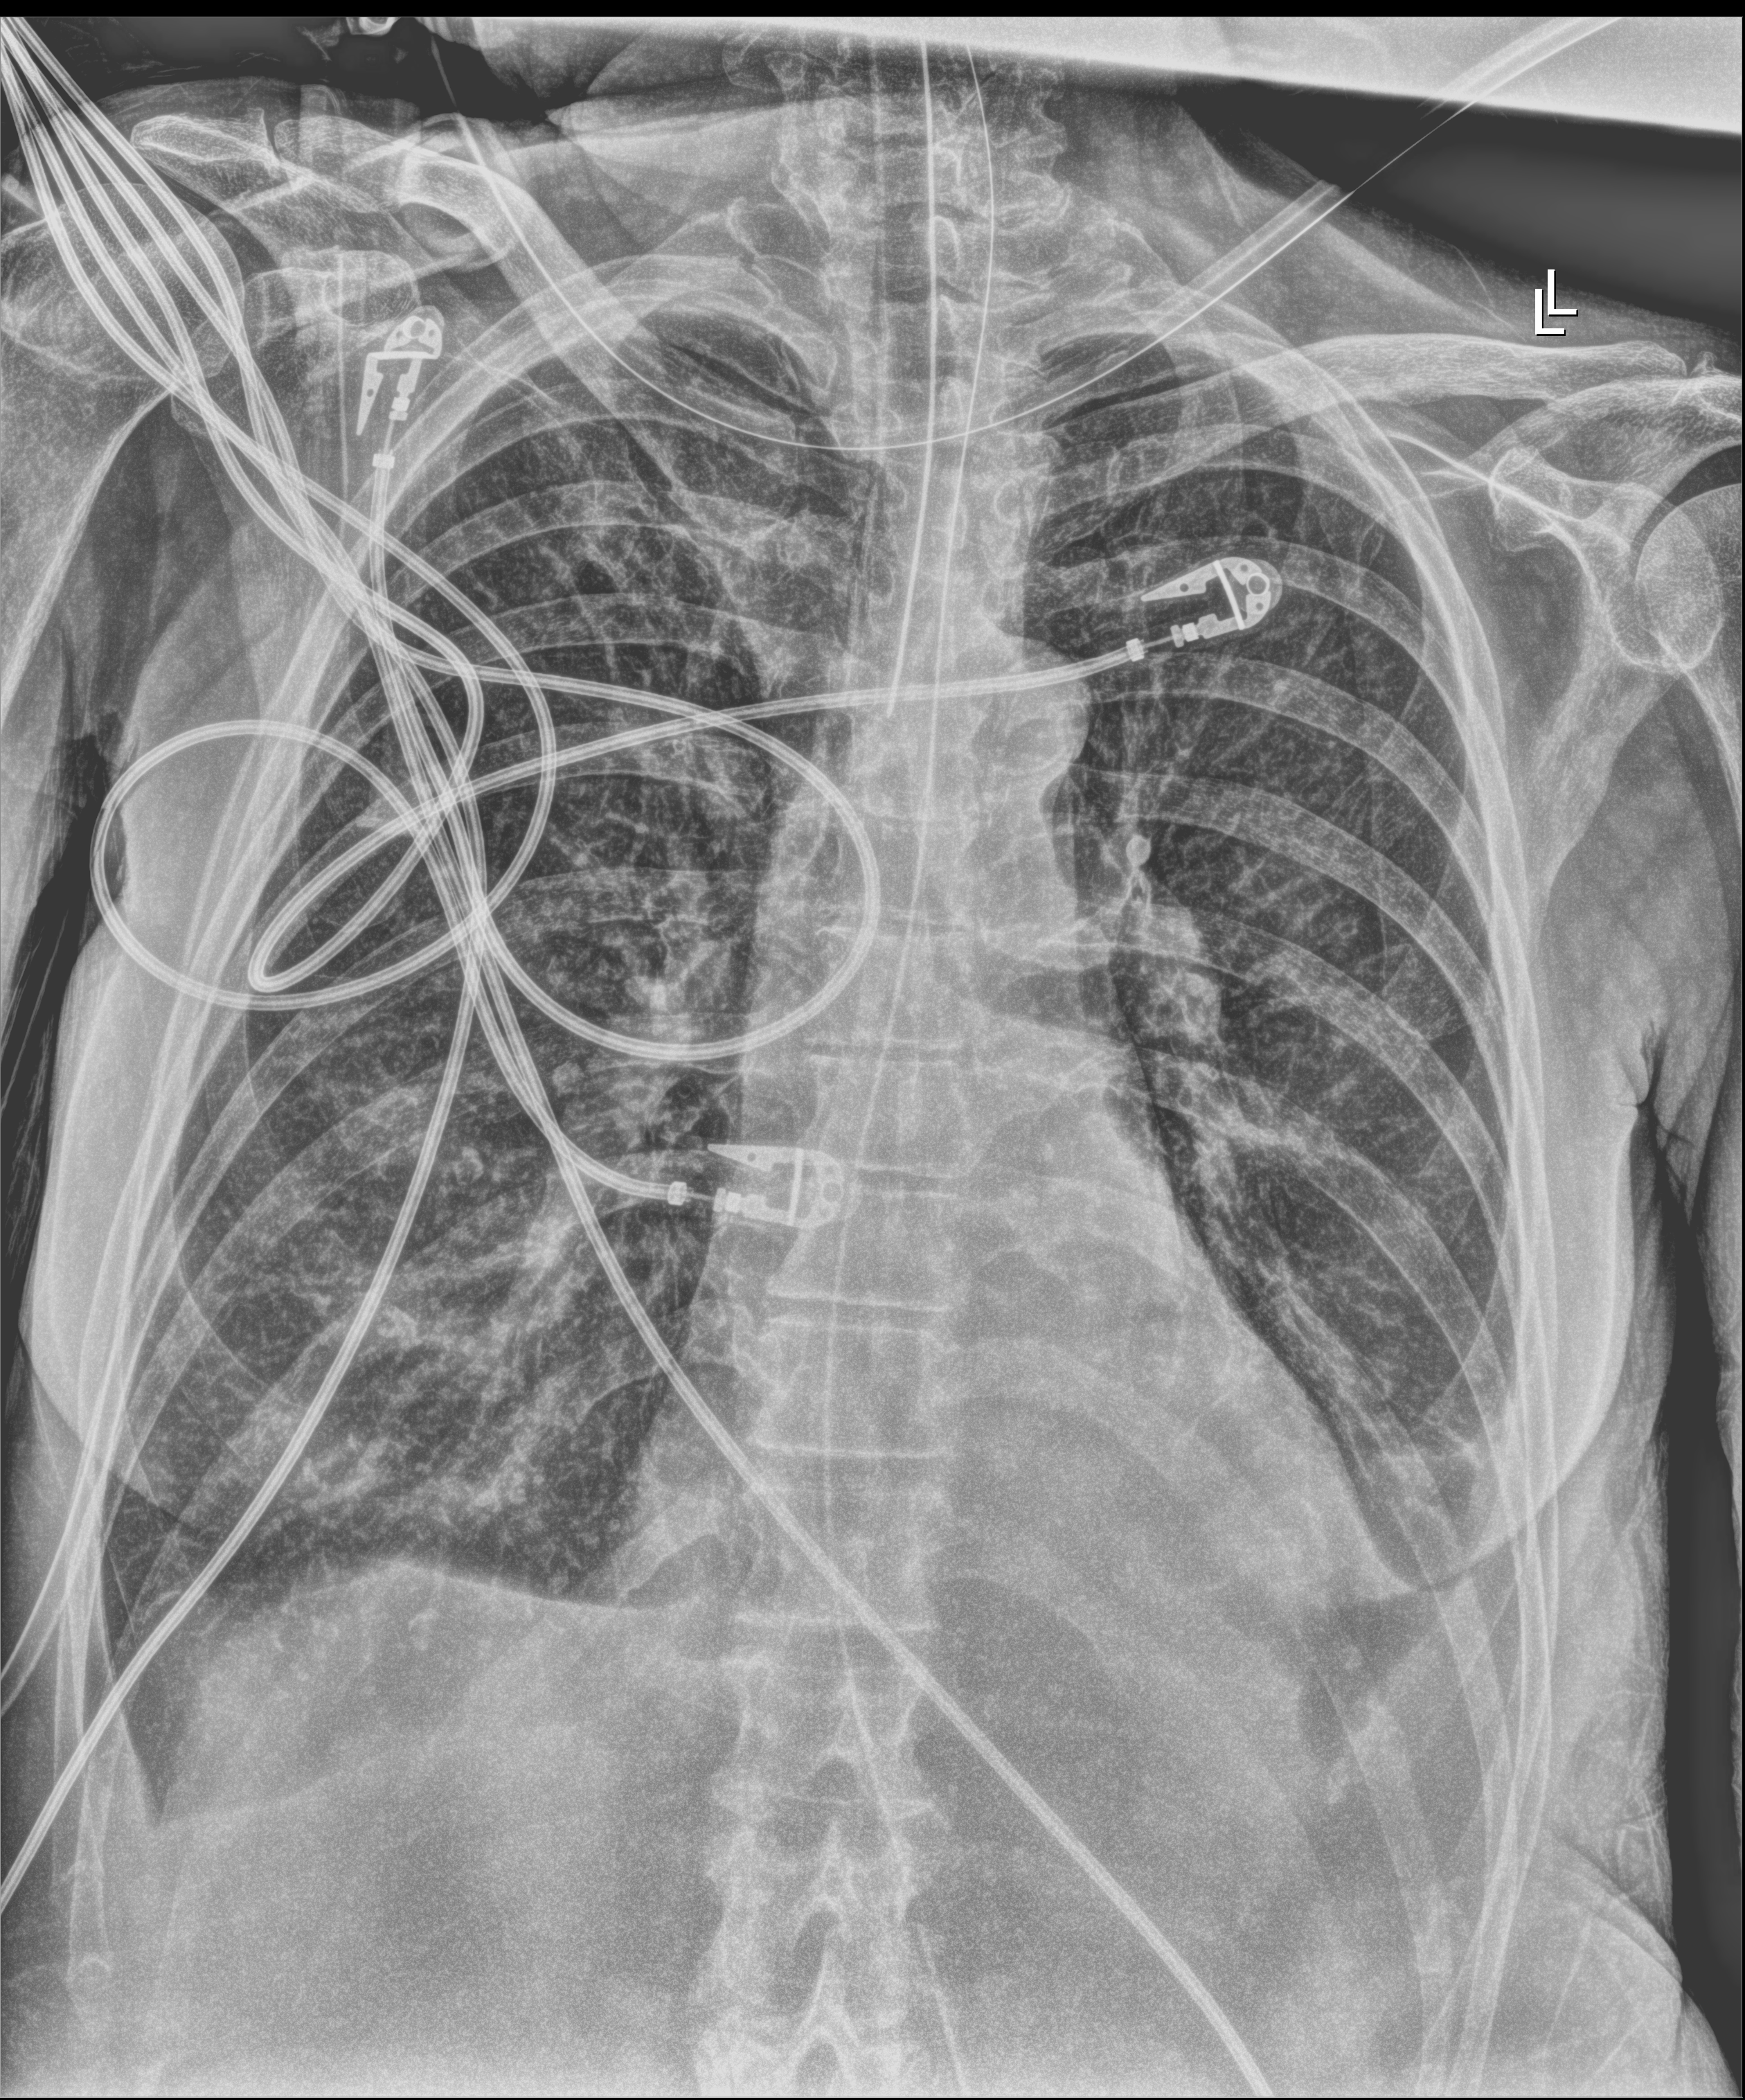
Chest radiograph, anteroposterior (AP) projection. Patient hospitalised with COVID-19; female, aged 60–74 years.
Admission-level facts for this patient (not findings on this image; timing relative to this image not recorded):
- mechanically ventilated during this hospital stay: yes